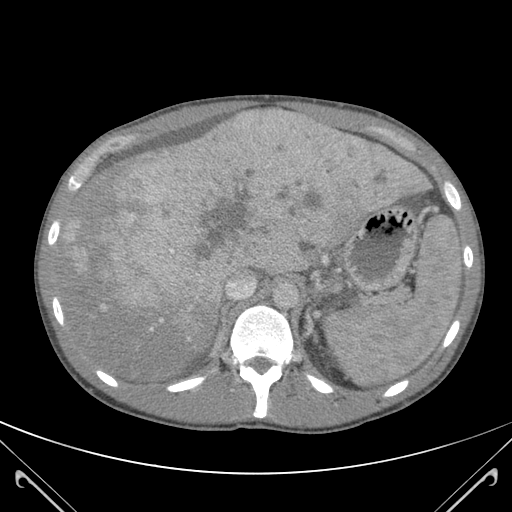
Contrast-enhanced abdominal CT (liver protocol), one axial slice; slice 83 of 118 in the series (ordered by position); soft-tissue window (W 400 / L 40 HU); 3 mm slice thickness; 512 × 512 image matrix, field of view 380 × 380 mm. Case-level facts recorded for this patient, not image findings: diagnosis: hepatocellular carcinoma (patient treated with transarterial chemoembolisation; whether this scan precedes or follows treatment is not stated here); TNM stage (as recorded): Stage-IIIB; Child-Pugh class: A; tumour nodularity: uninodular.
Structures marked on this image (semi-automatic segmentation, software-assisted and operator-edited):
- abdominal aorta: box from (x=273, y=284) to (x=298, y=308) px
- liver parenchyma outside the tumour (the mass and vessels are separate outlines, so this box may not span the whole liver): (x=60, y=115)–(x=423, y=378)
- mass: (x=91, y=118)–(x=413, y=332)
- liver vessels: (x=67, y=116)–(x=418, y=340)